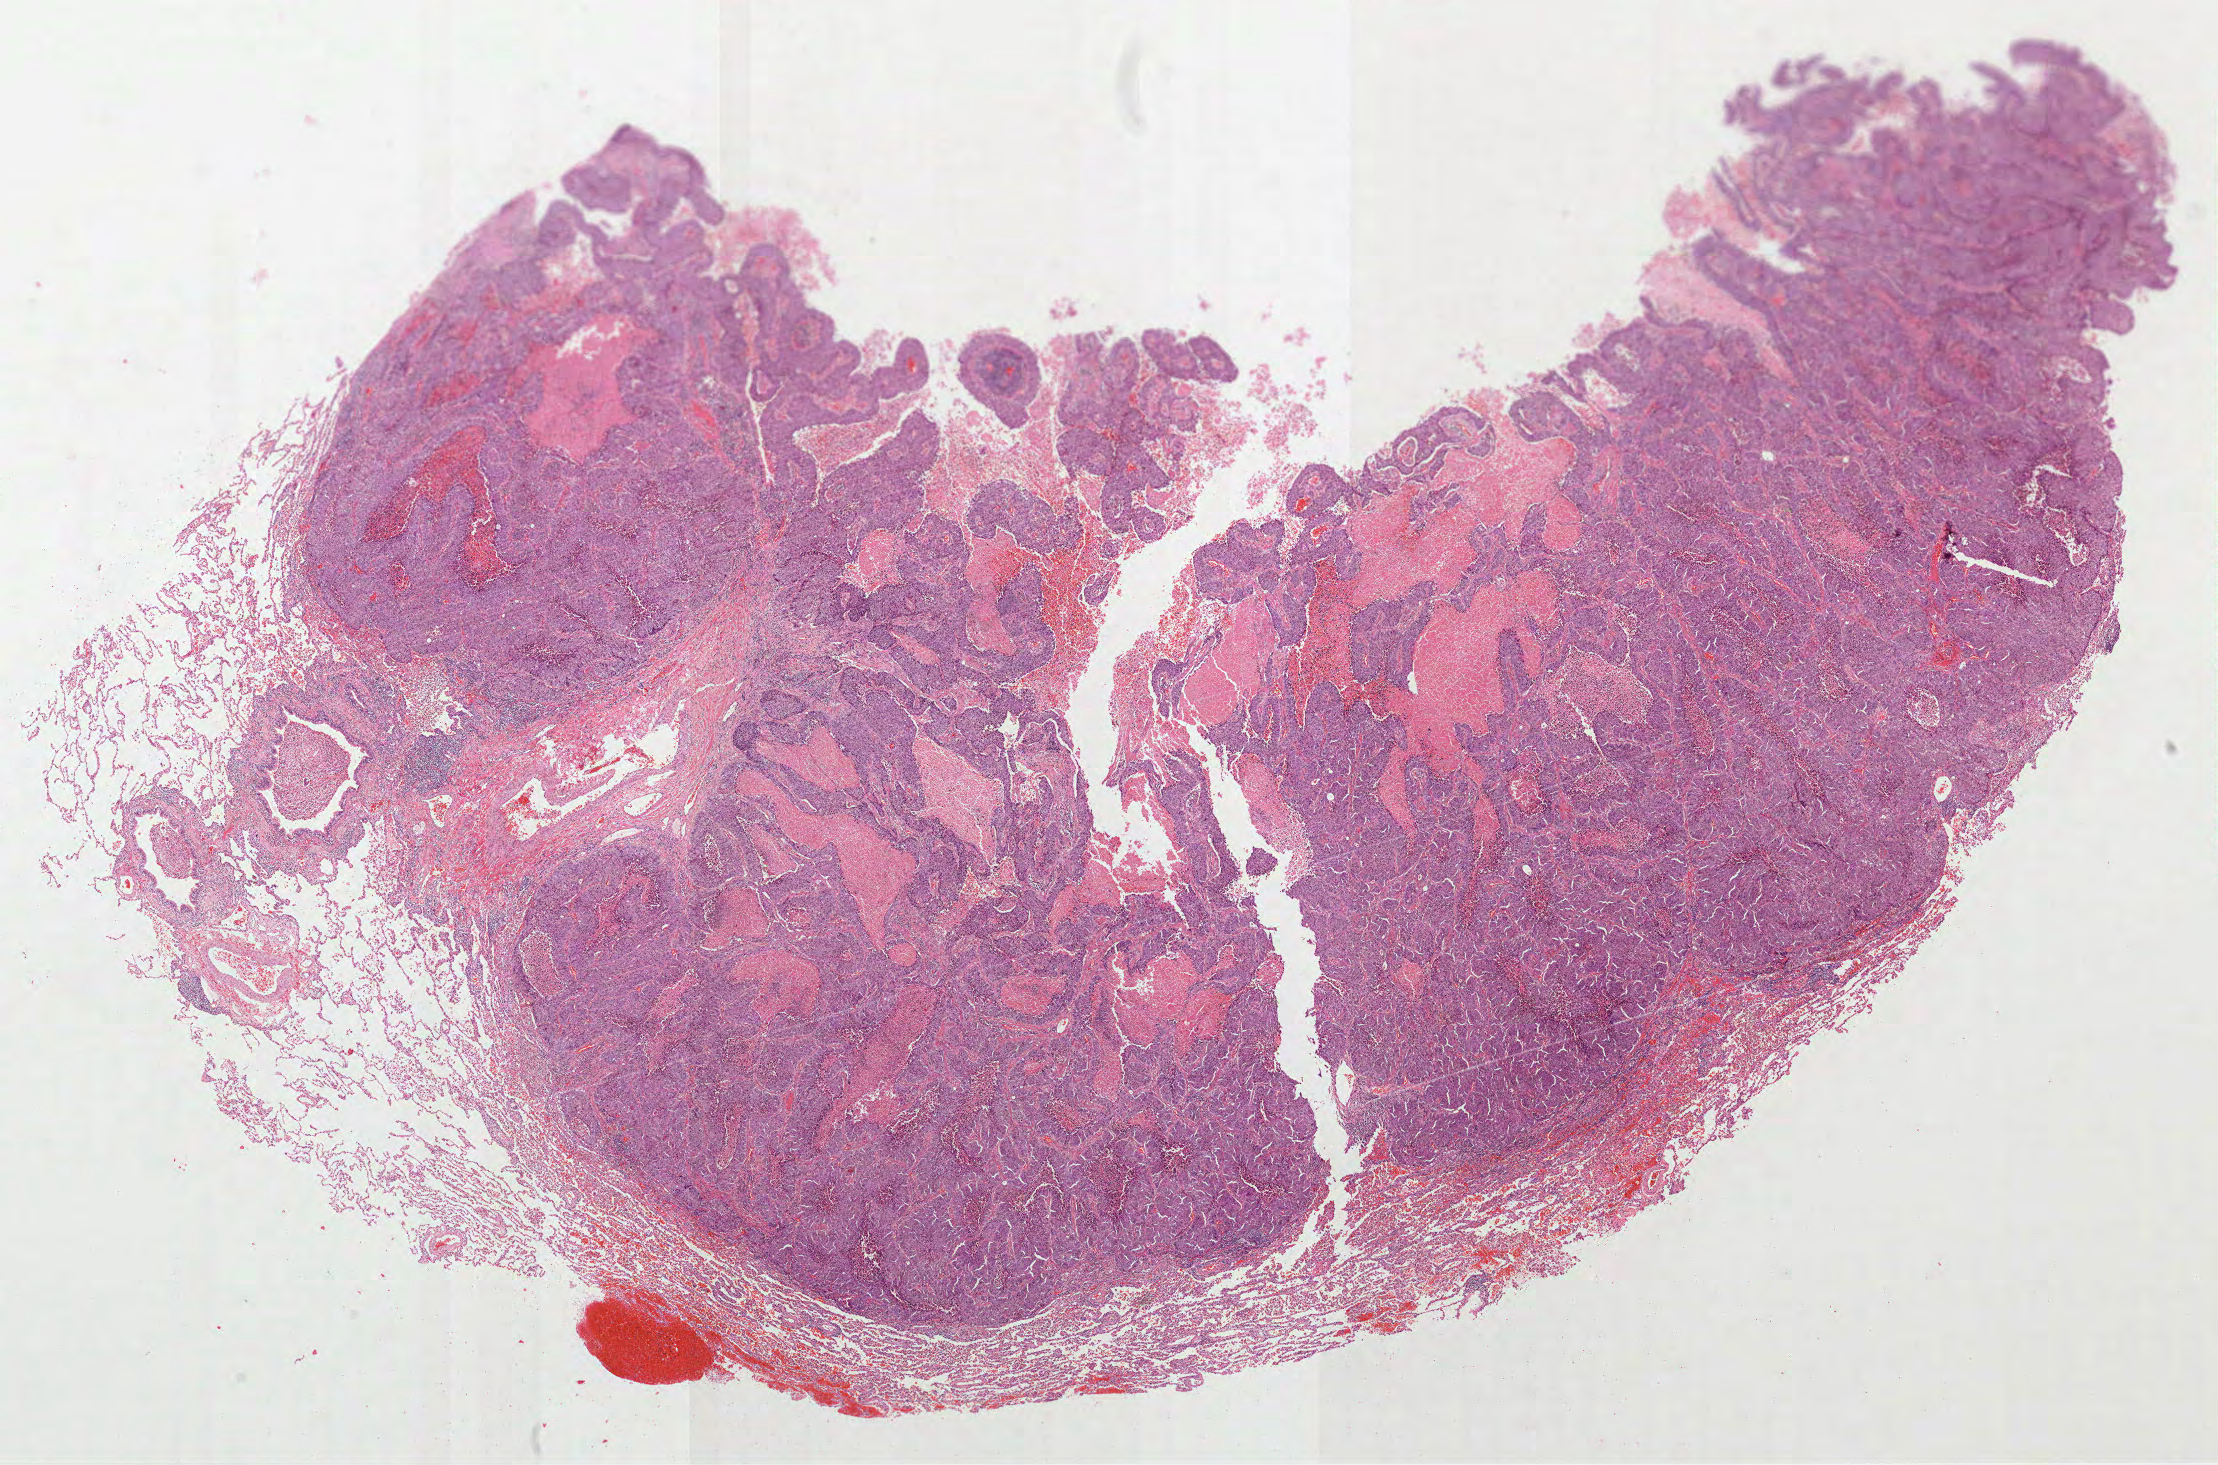
H&E-stained whole-slide image — whole scanned area (about 17.9 x 11.8 mm, slide scanned at 40x) shown as a low-resolution overview, formalin-fixed paraffin-embedded (FFPE) diagnostic section, sample: primary tumour, lung. Male, age 53 years at initial diagnosis.
AJCC pathologic stage: IB (7th edition). Histologic diagnosis: Squamous cell carcinoma, NOS.